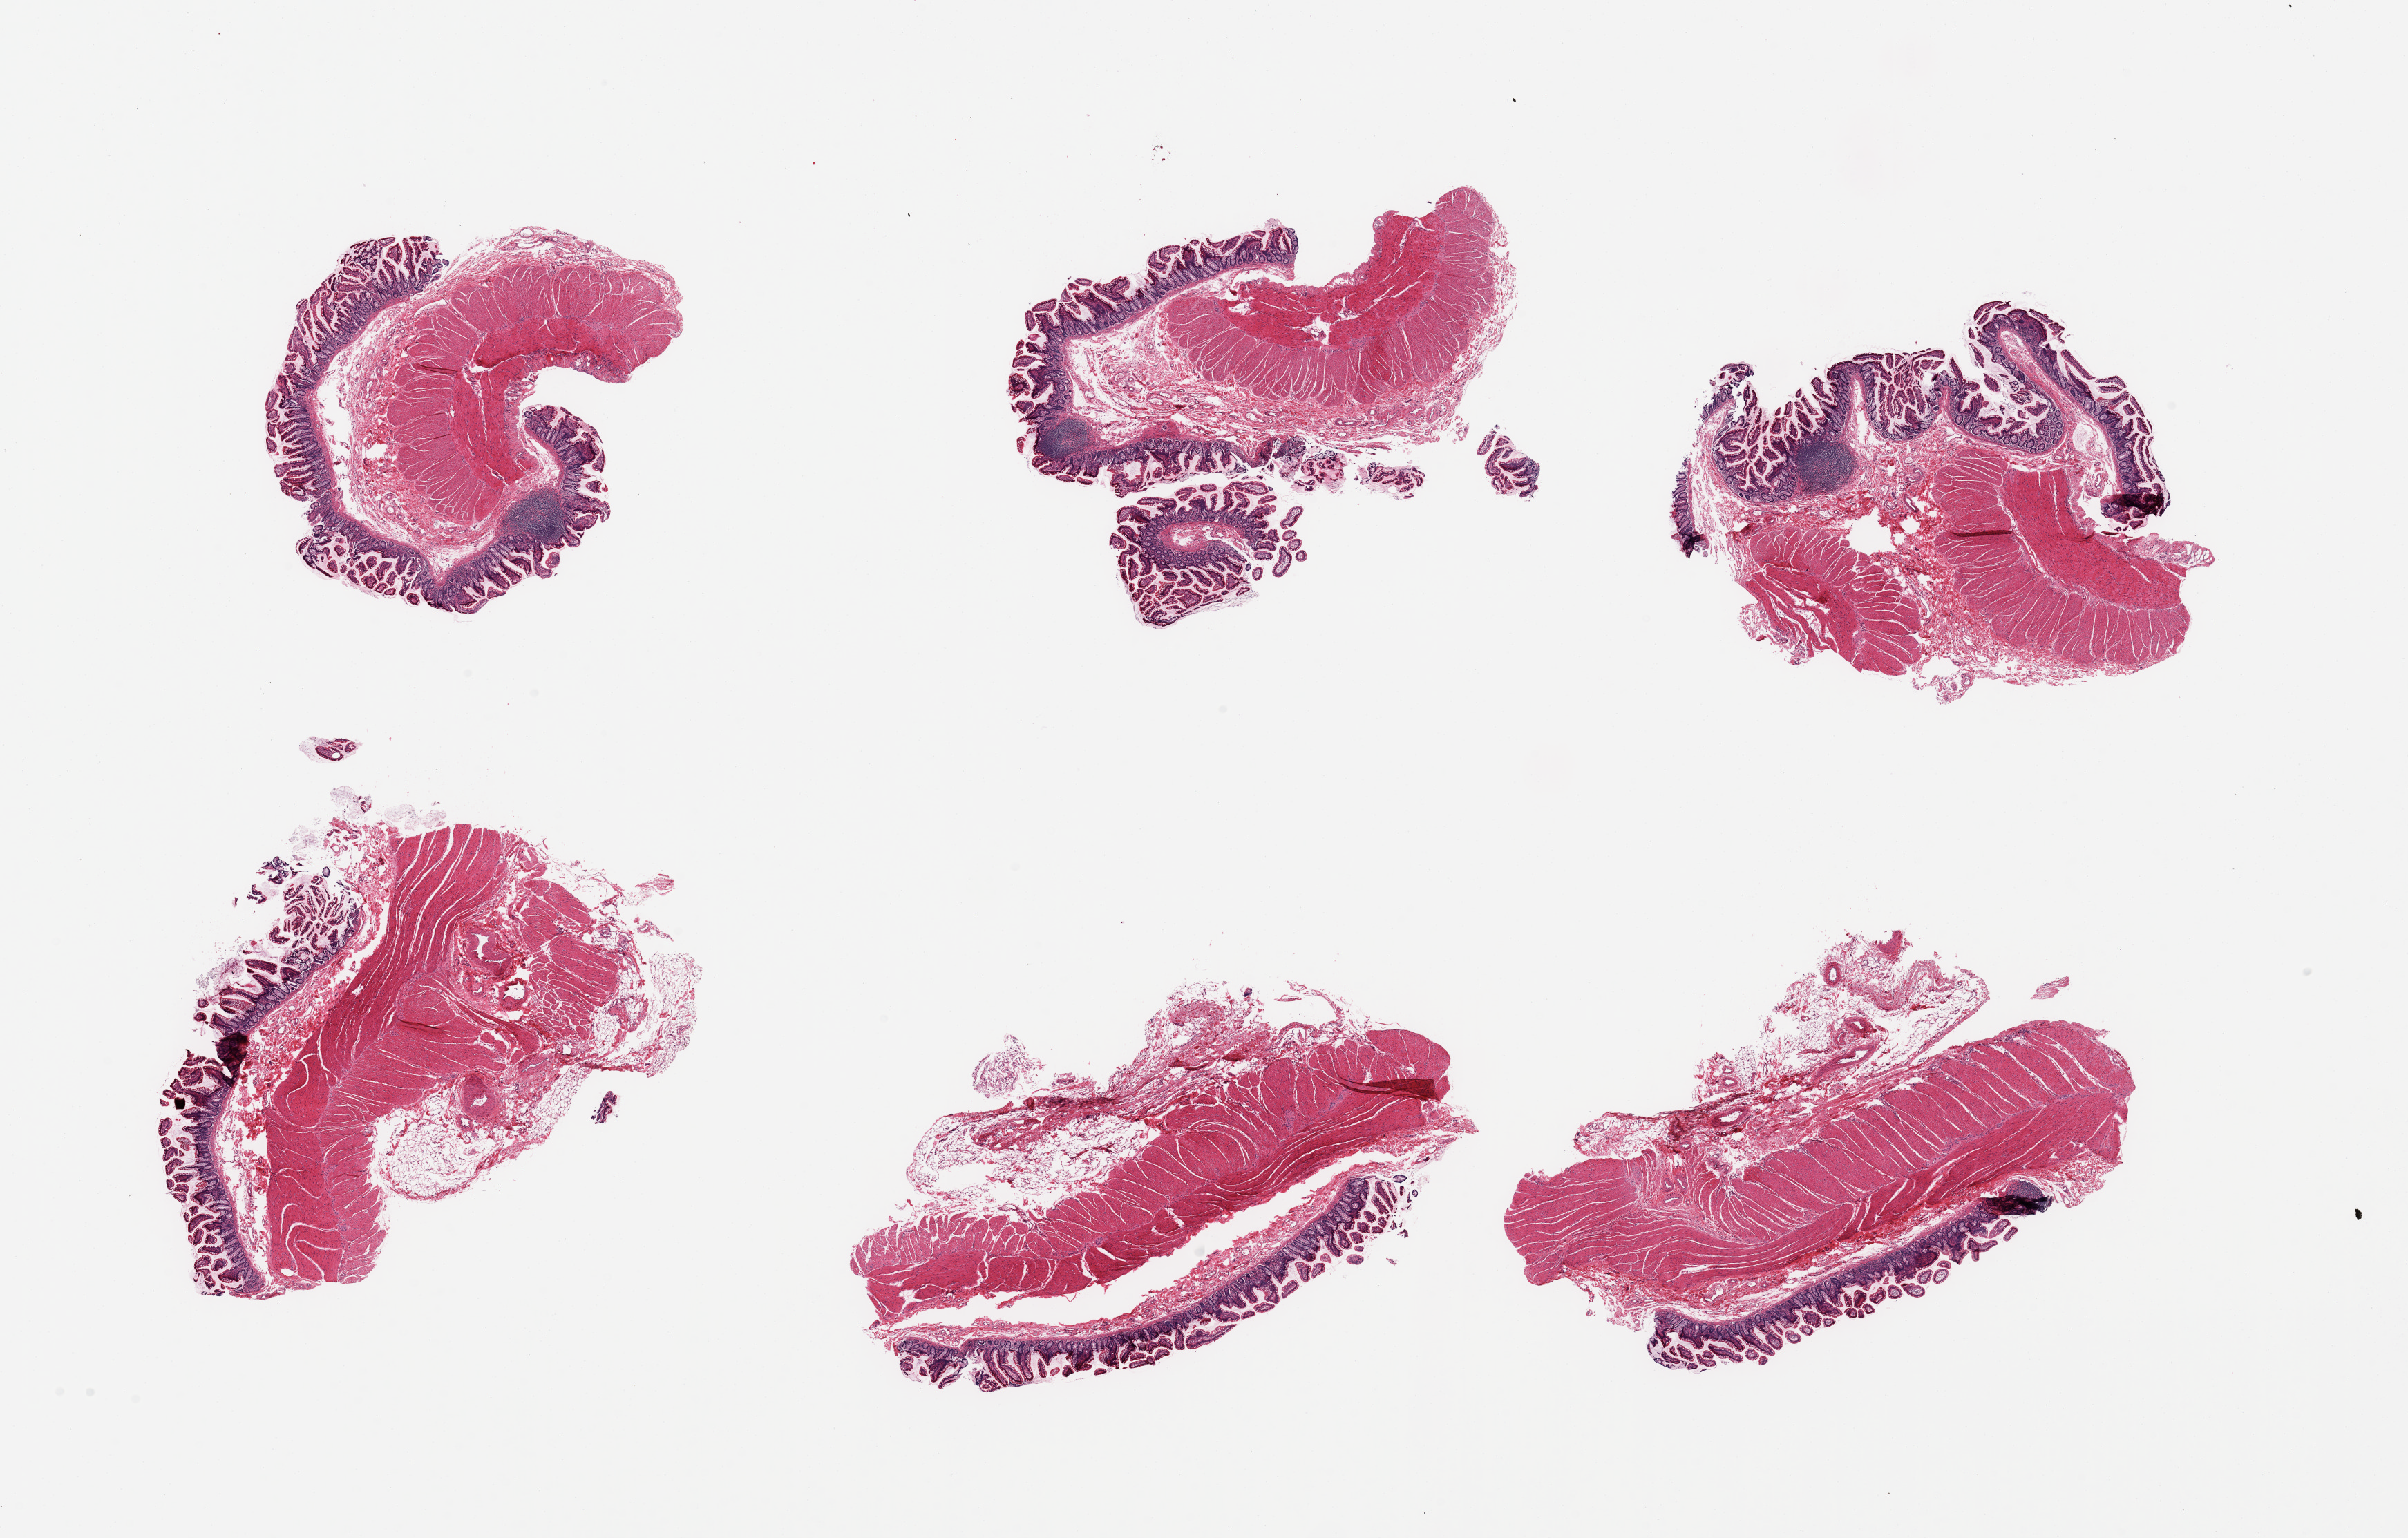
H&E whole-slide image, a low-resolution overview of the entire scanned area, about 27.6 x 17.6 mm (acquisition: 20x scan); PAXgene-fixed, paraffin-embedded tissue; target tissue: ileum; donor tissue sample. Donor: male.
- reviewer comment on this tissue sample: 6 pieces, ~15% target lymphoid aggregates